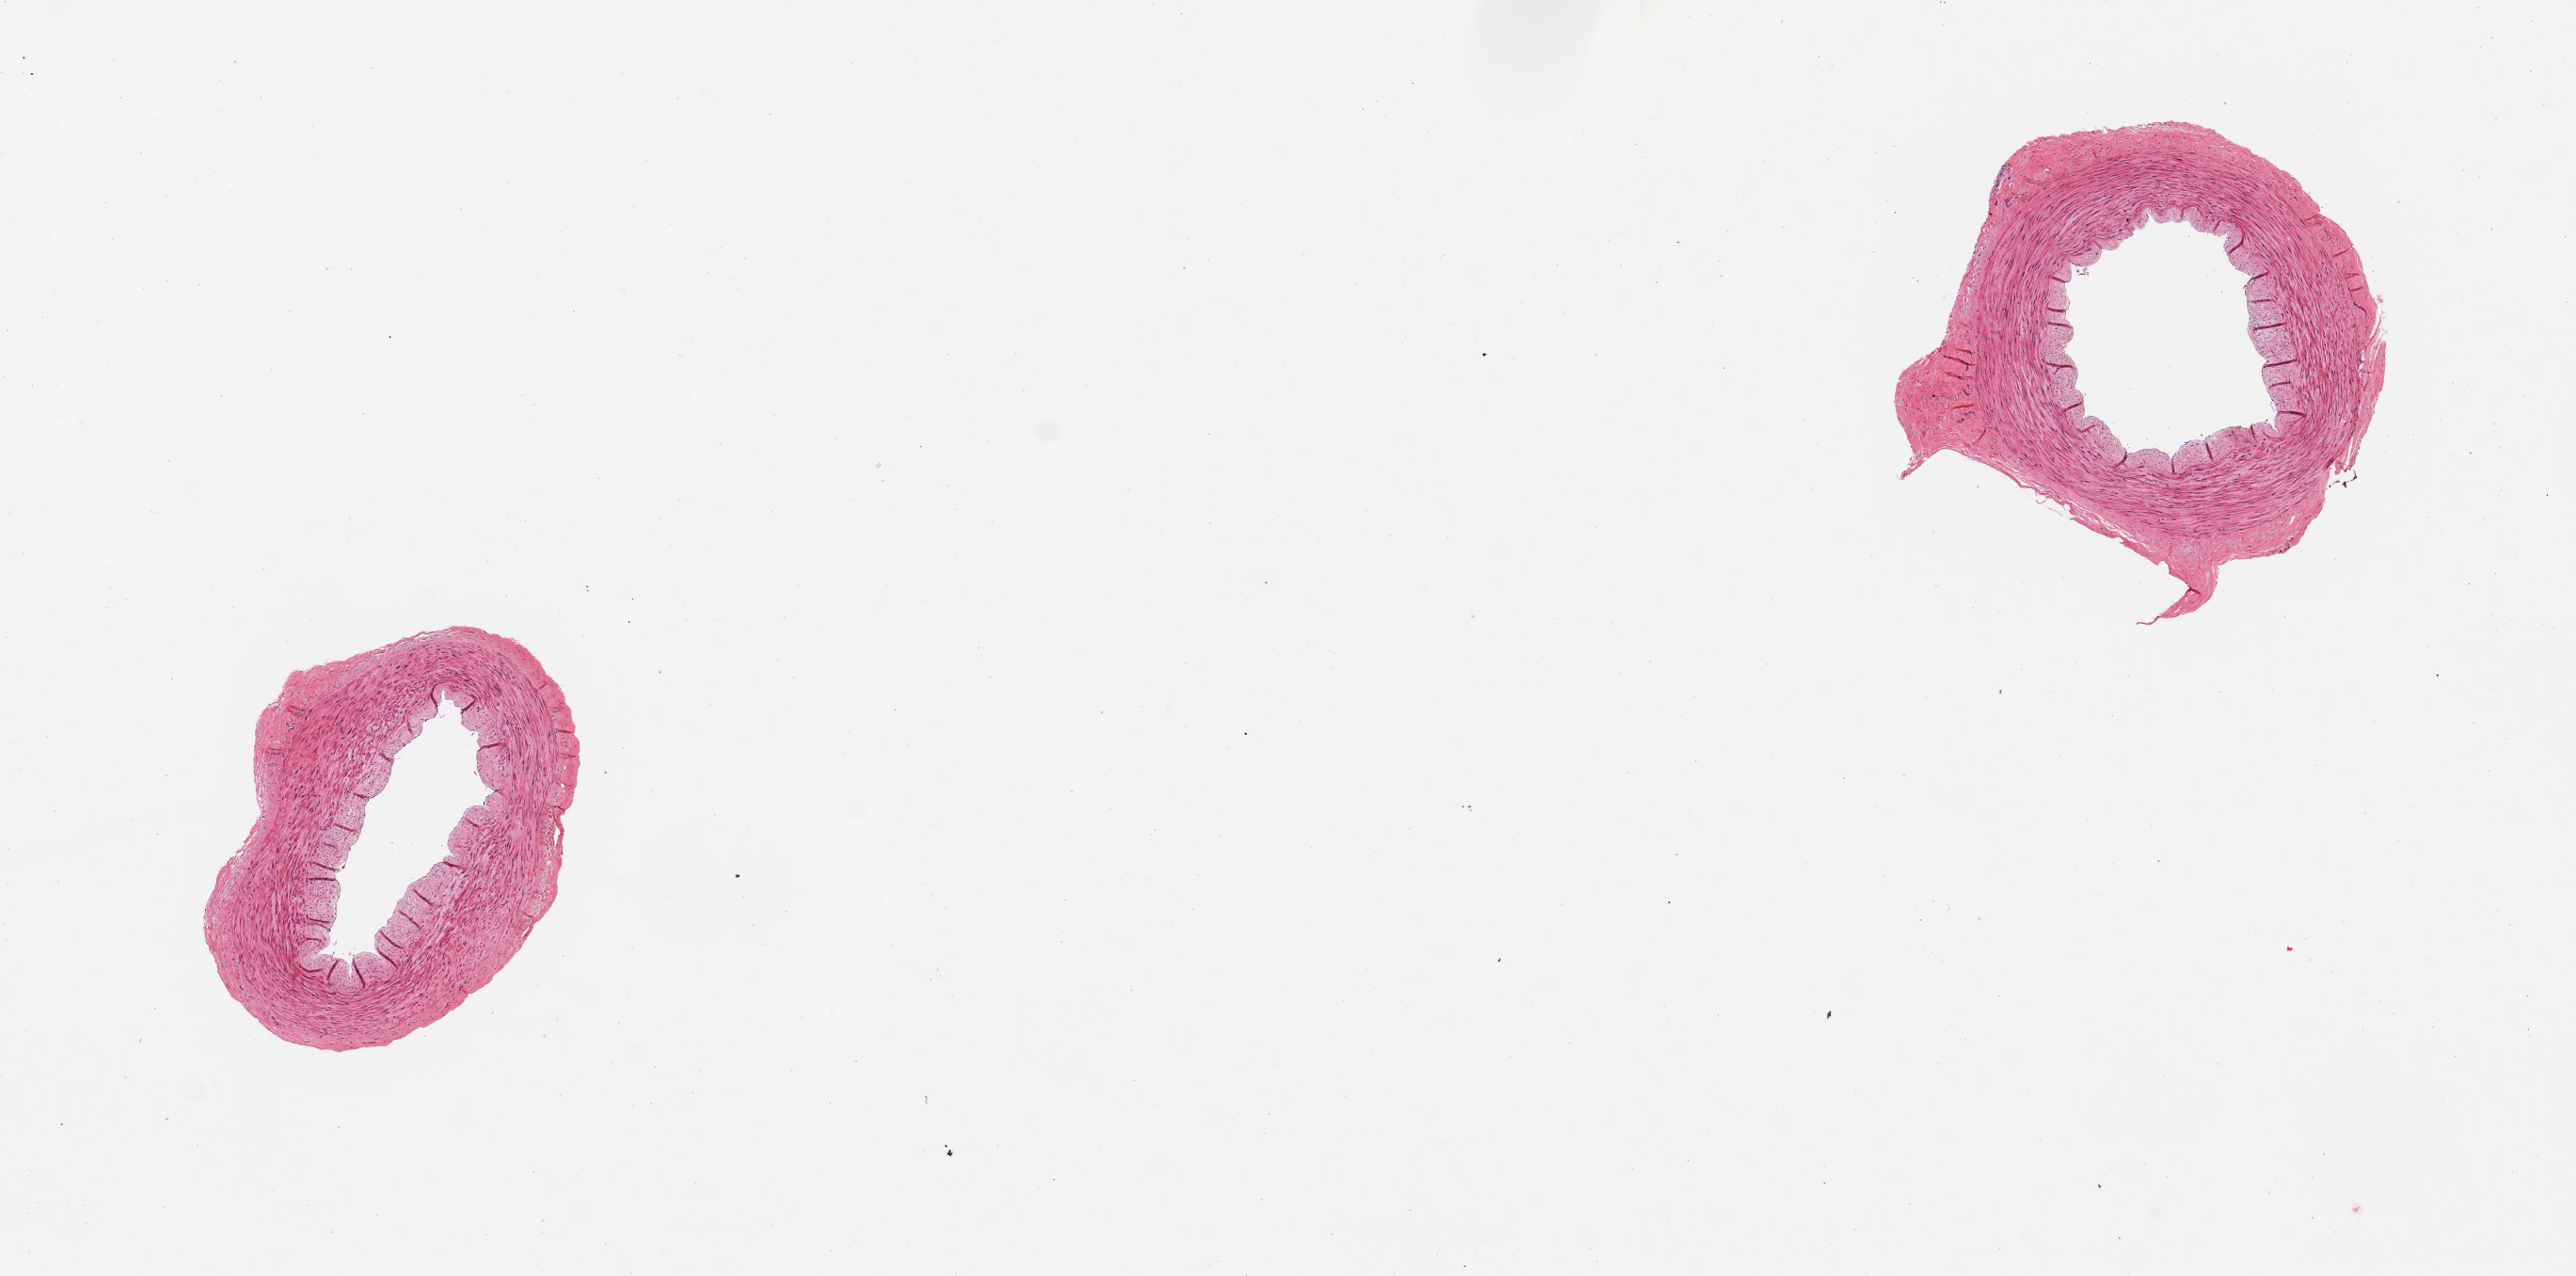
Digitized hematoxylin and eosin (H&E)-stained section — shown as a low-resolution overview of the whole scanned area (about 10.8 x 5.4 mm), PAXgene-fixed paraffin-embedded (PFPE) section, section of tibial artery (target tissue), tissue donor sample. Male donor.
Pathologist's review note for this sample: 2 pieces; well trimmed, no external fat; no lesions.